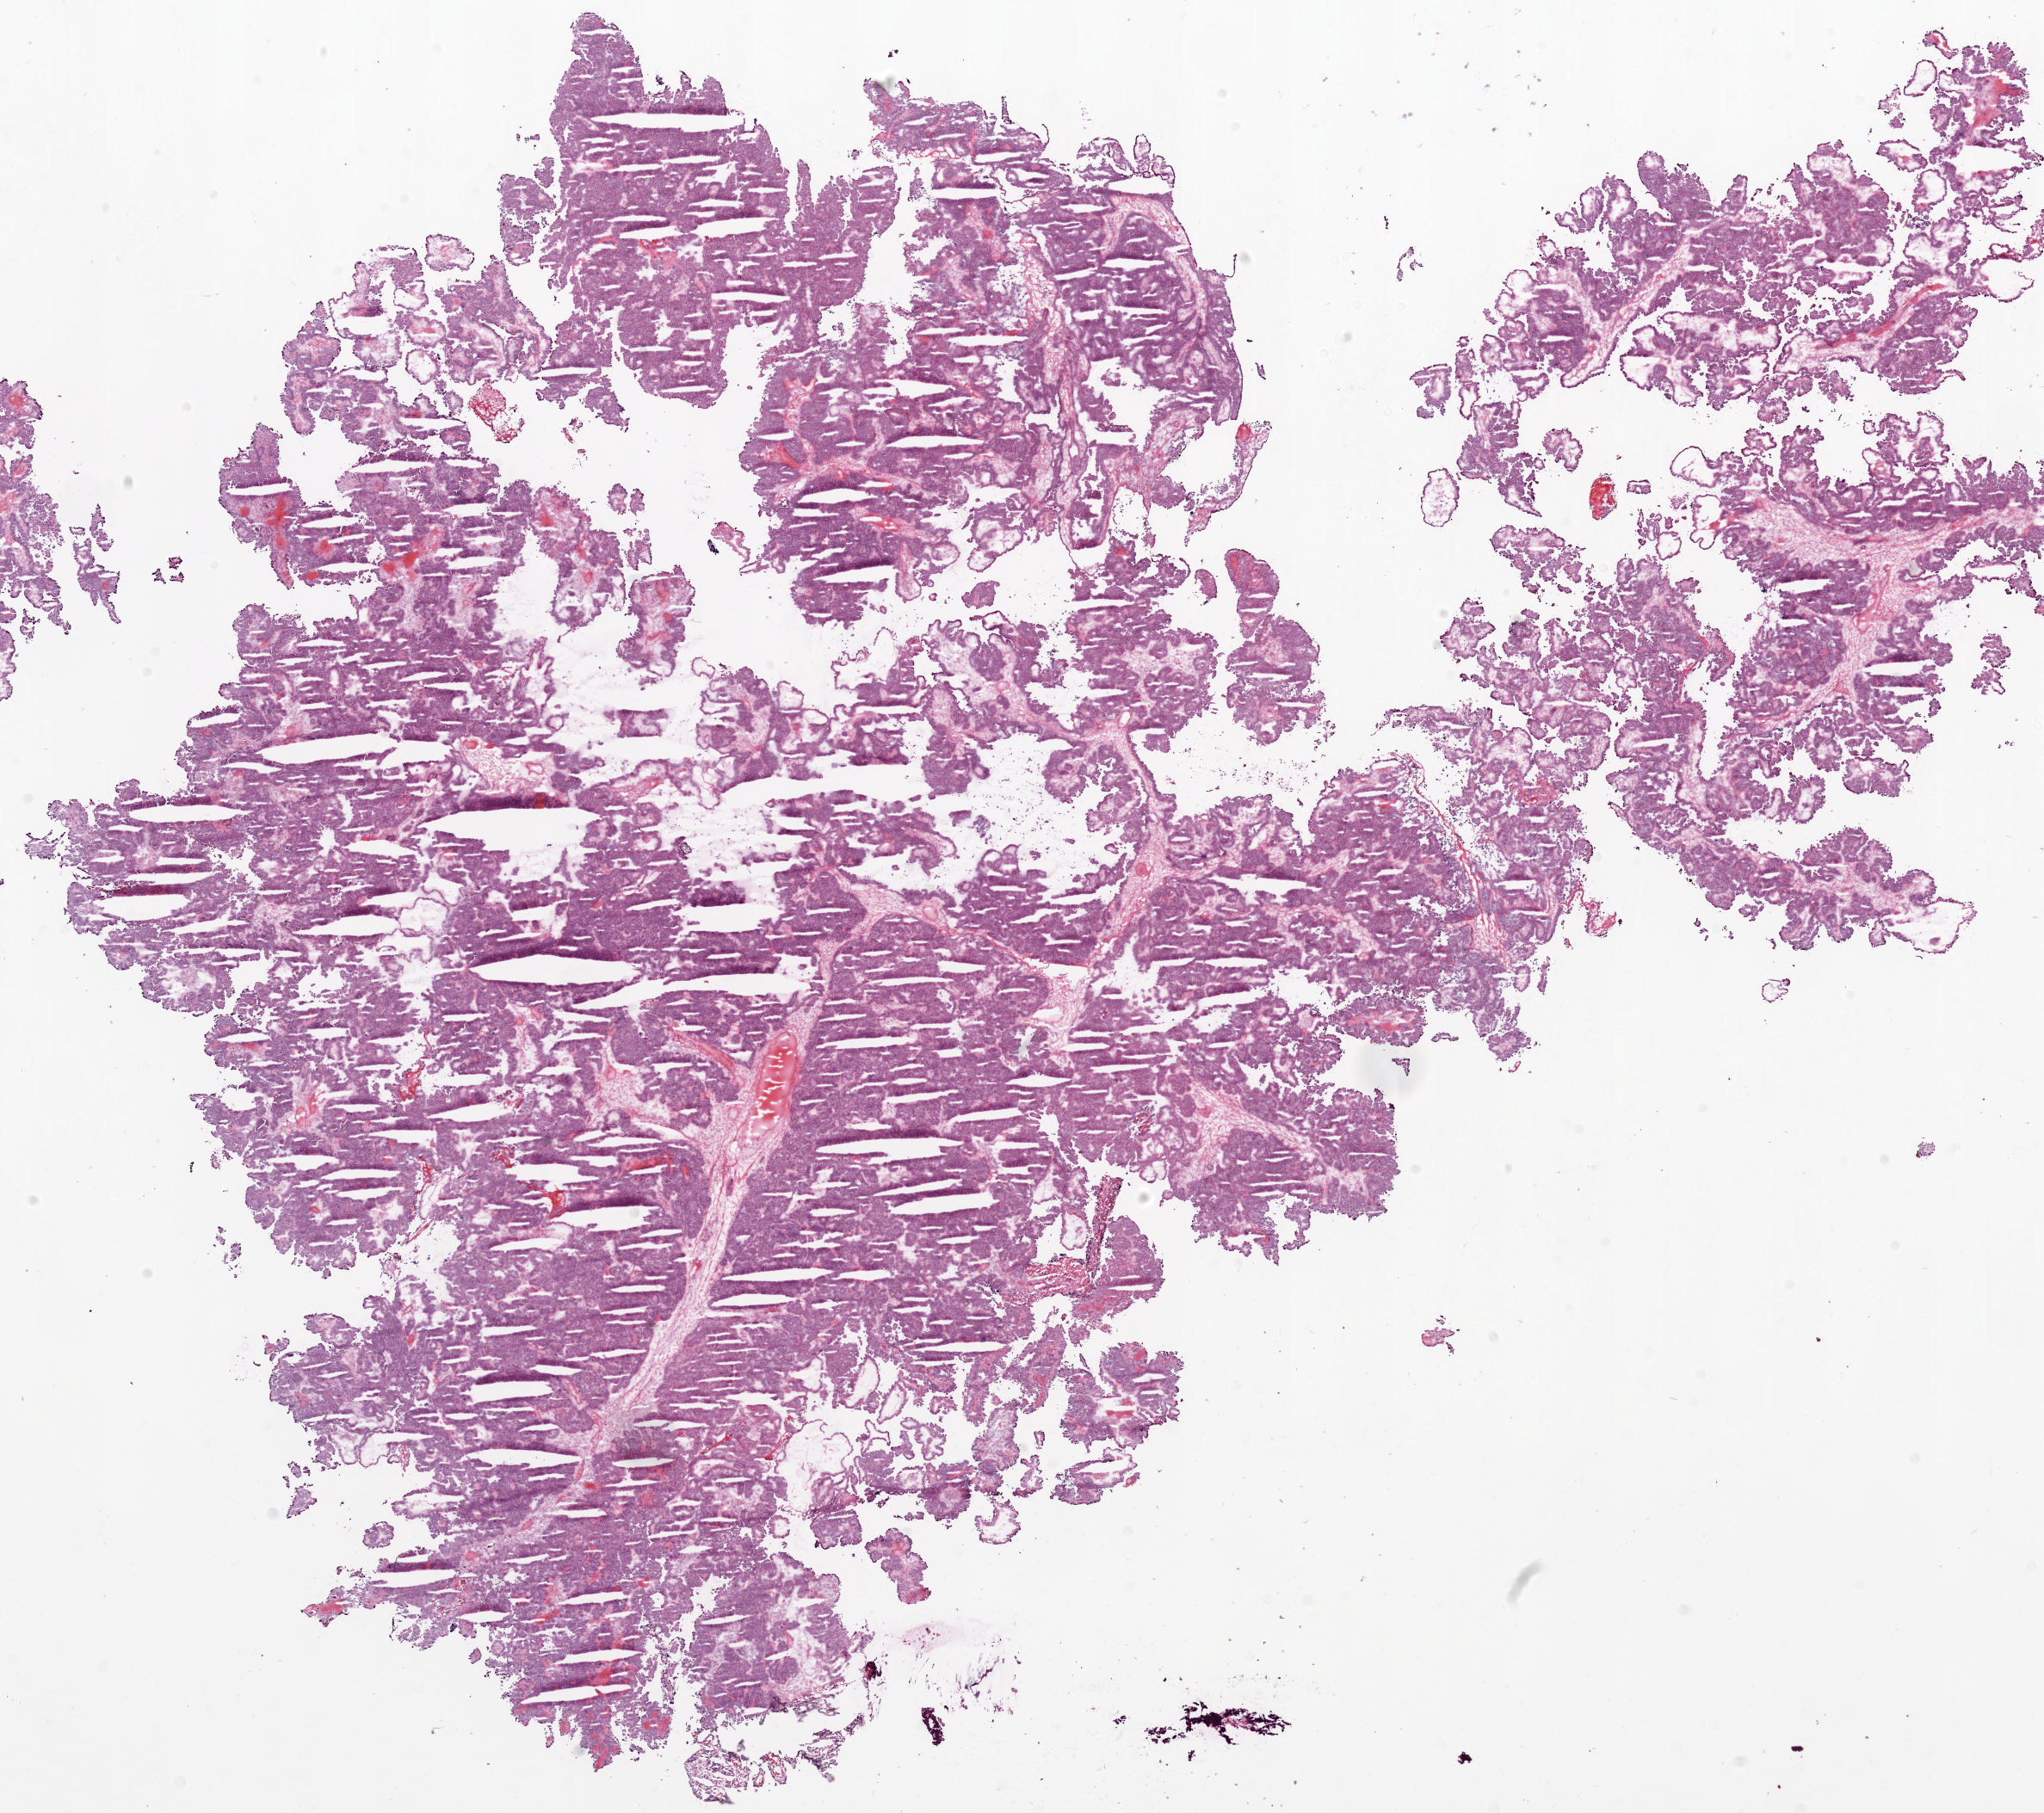
H&E whole-slide image — shown as a low-resolution overview of the whole scanned area (about 19.1 x 16.9 mm), frozen section from the top of the tissue portion, primary tumour sample from the ovary. Female, age 68 years at initial diagnosis. Histologic grade: G3 (poorly differentiated). Composition of this section per pathologist review: tumour cells 94%, tumour nuclei 95%, normal cells 0%, stromal cells 5%, necrosis 1%.
Histologic diagnosis: Serous cystadenocarcinoma, NOS. FIGO stage: IV.